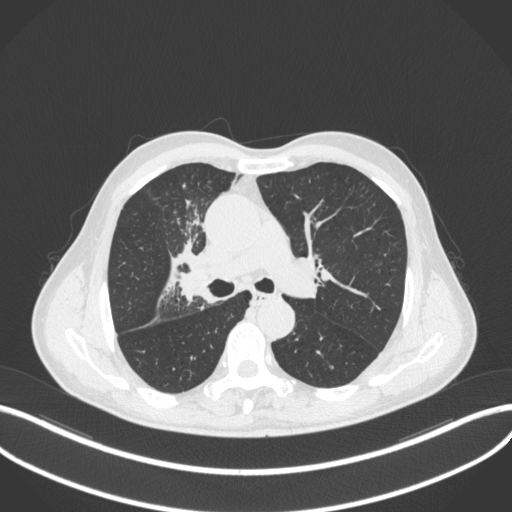
Chest CT, one axial slice. Position 305 of 490 along the scan axis. Reconstruction kernel B31f. 120 kVp. Lung window (W 1500 / L -600 HU). 512 × 512 image matrix, field of view 400 × 400 mm. Male patient, age 69 years. From the clinical record (not read from this slice): clinical TNM (as recorded): T2a N0 M0.
Structures marked on this image (bounding box drawn by a radiologist):
- lung tumour (recorded histology: adenocarcinoma): bounding box (x1, y1, x2, y2) in pixels: (175, 264, 201, 304)